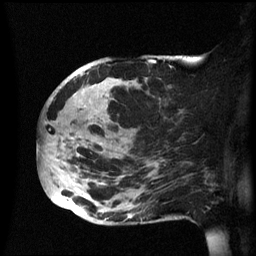
Breast MRI (dynamic contrast-enhanced), one sagittal slice; position 26 of 60 along the scan axis; dynamic contrast-enhanced series, image 2 of 3 at this slice position (ordered by acquisition); 1.5 T; TE 4.2 ms, TR 8.4 ms; 2.4 mm slice thickness; 256 × 256 image matrix. Patient: female, 49 years.
Structures marked on this image (semi-automatically segmented with operator editing):
- analysis volume of interest (the breast-tissue region the enhancement analysis was run in; not a lesion): bounding box [x1, y1, x2, y2] px = [39, 56, 174, 225]
- tumour enhancement mask (voxels above the 70 % enhancement threshold inside the analysis volume of interest): [44, 74, 135, 185]